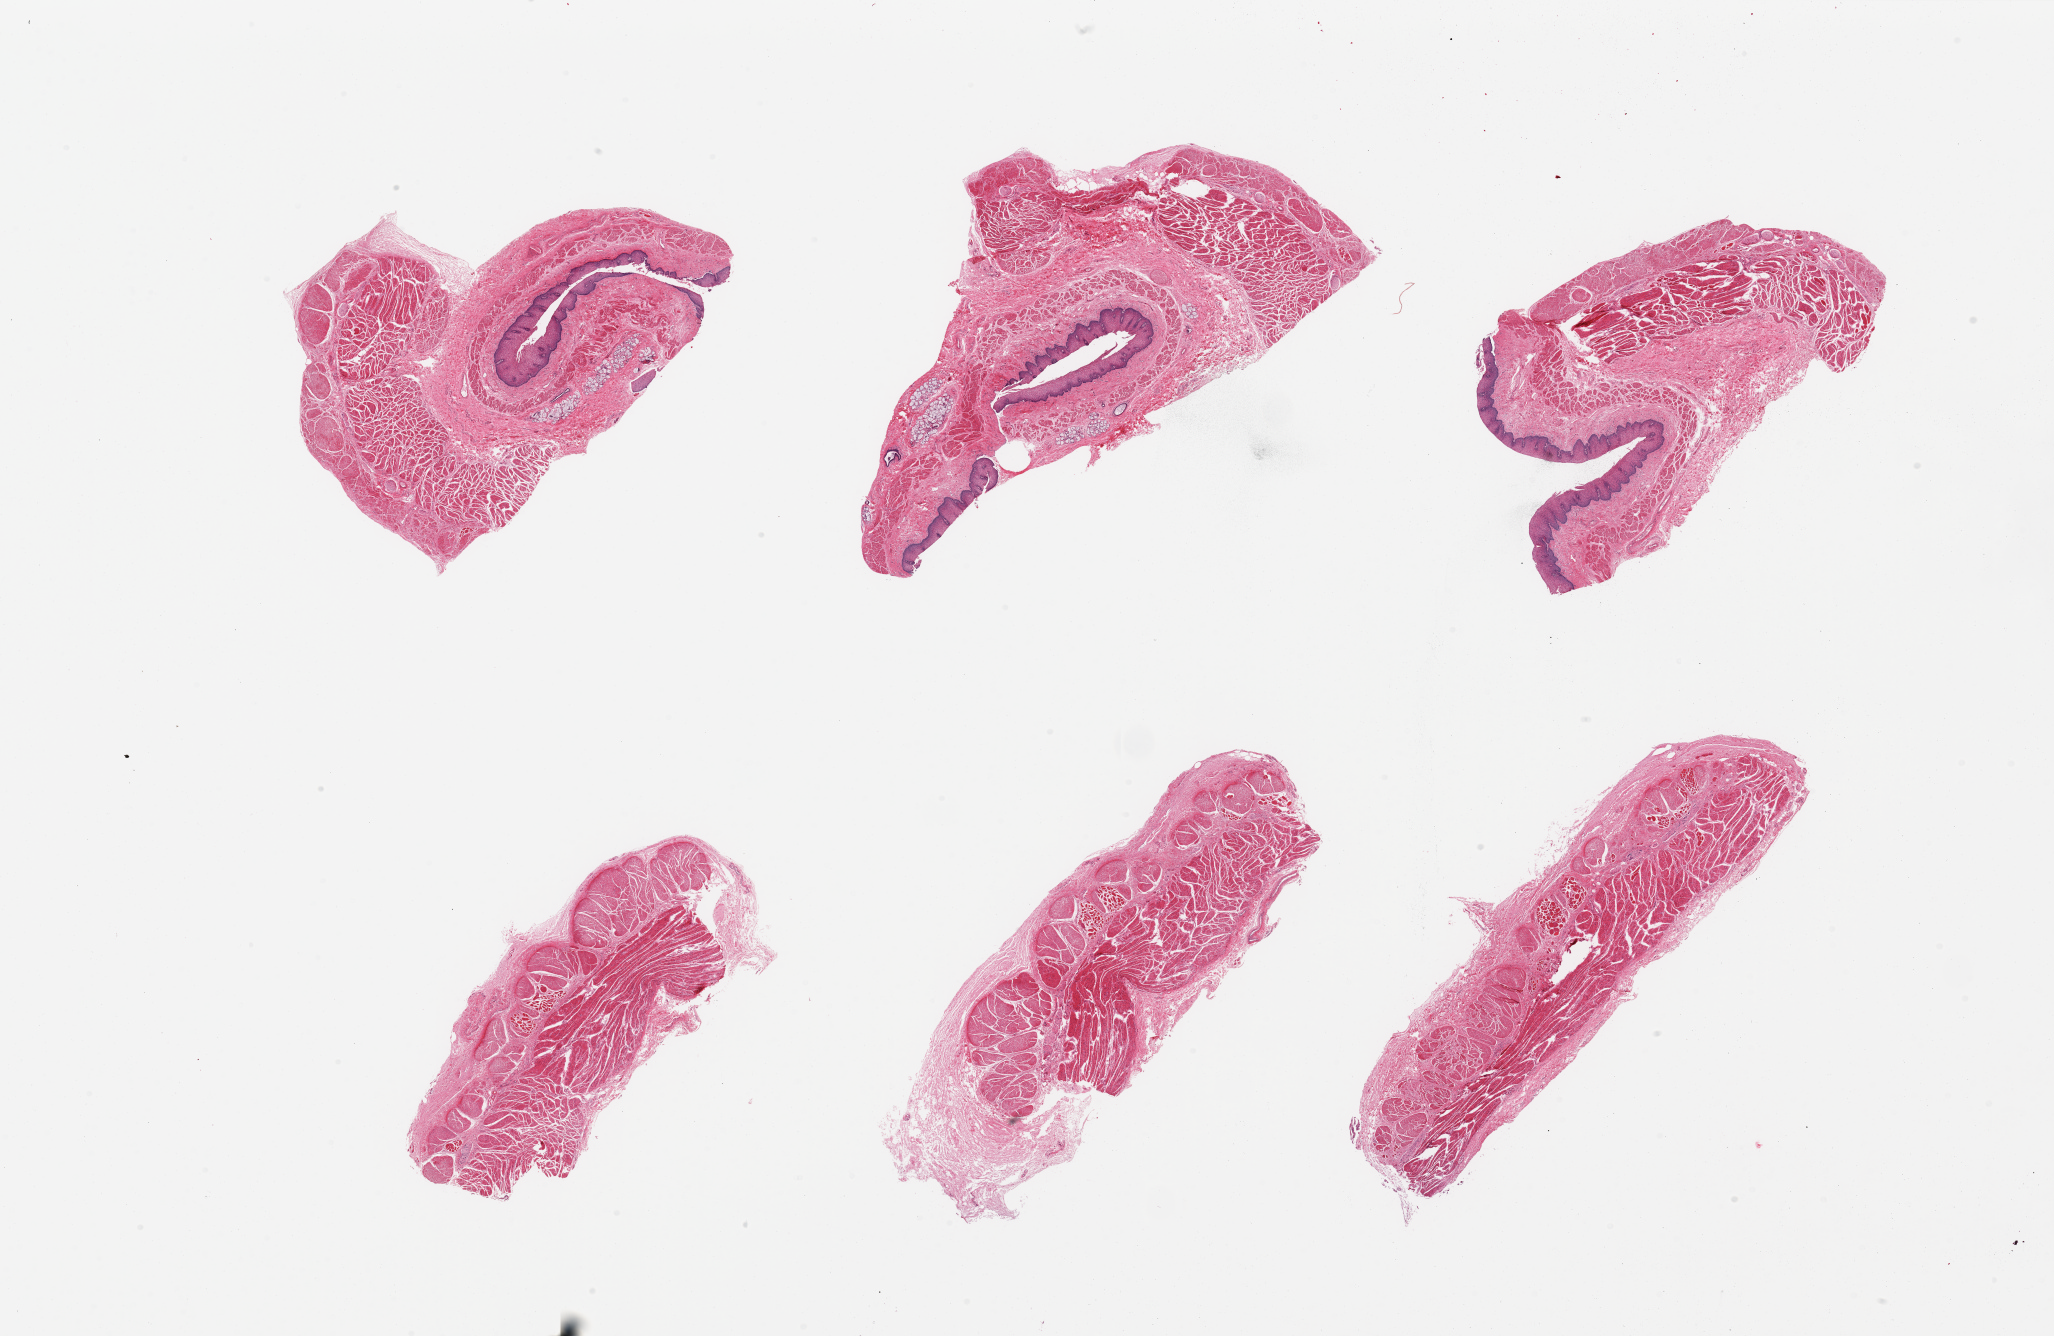
Digitized hematoxylin and eosin (H&E)-stained section, brightfield — whole scanned area (about 32.5 x 21.1 mm) shown as a low-resolution overview, PAXgene-fixed, paraffin-embedded tissue, sampled site (target tissue): aorta, tissue donor sample. Male donor.
Reviewer comment on this tissue sample: 6 pieces, sections of smooth muscle/squamous mucosa.